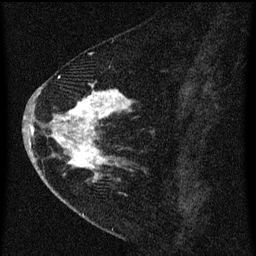
Breast MRI (dynamic contrast-enhanced), one sagittal slice. Position 25 of 60 along the scan axis. Dynamic contrast-enhanced series, image 2 of 3 at this slice position (ordered by acquisition). 1.5 T. TE 4.2 ms, TR 8 ms. 2 mm slice thickness. 256 × 256 image matrix, field of view 180 × 180 mm. Patient: female, 47 years.
Outlined on this slice (semi-automatically segmented with operator editing):
- analysis volume of interest (the breast-tissue region the enhancement analysis was run in; not a lesion): bounding box [x1, y1, x2, y2] px = [38, 76, 143, 193]
- tumour enhancement mask (voxels above the 70 % enhancement threshold inside the analysis volume of interest): [42, 78, 134, 183]